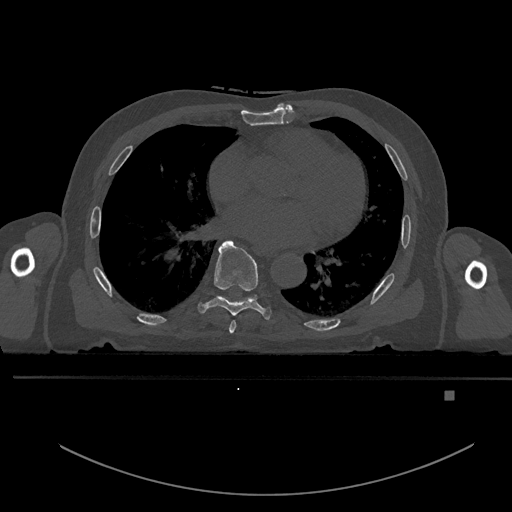
CT including the spine, one axial slice; slice 252 of 969 in the series (ordered by position); bone window (W 1800 / L 400 HU); 0.5 mm slice thickness; 512 × 512 image matrix, field of view 456 × 456 mm. Patient: male, 82 years. Case-level facts recorded for this patient, not image findings: primary cancer: prostate; vertebrae with lytic lesions (as recorded): T11, T9, T8, T2.
Annotated regions visible in this slice (semi-automatic segmentation, software-assisted and operator-edited):
- T6 vertebra: bounding box (x1, y1, x2, y2) in pixels: (229, 320, 236, 334)
- T7 vertebra: (198, 240, 272, 320)
- T8 vertebra: (220, 295, 257, 302)